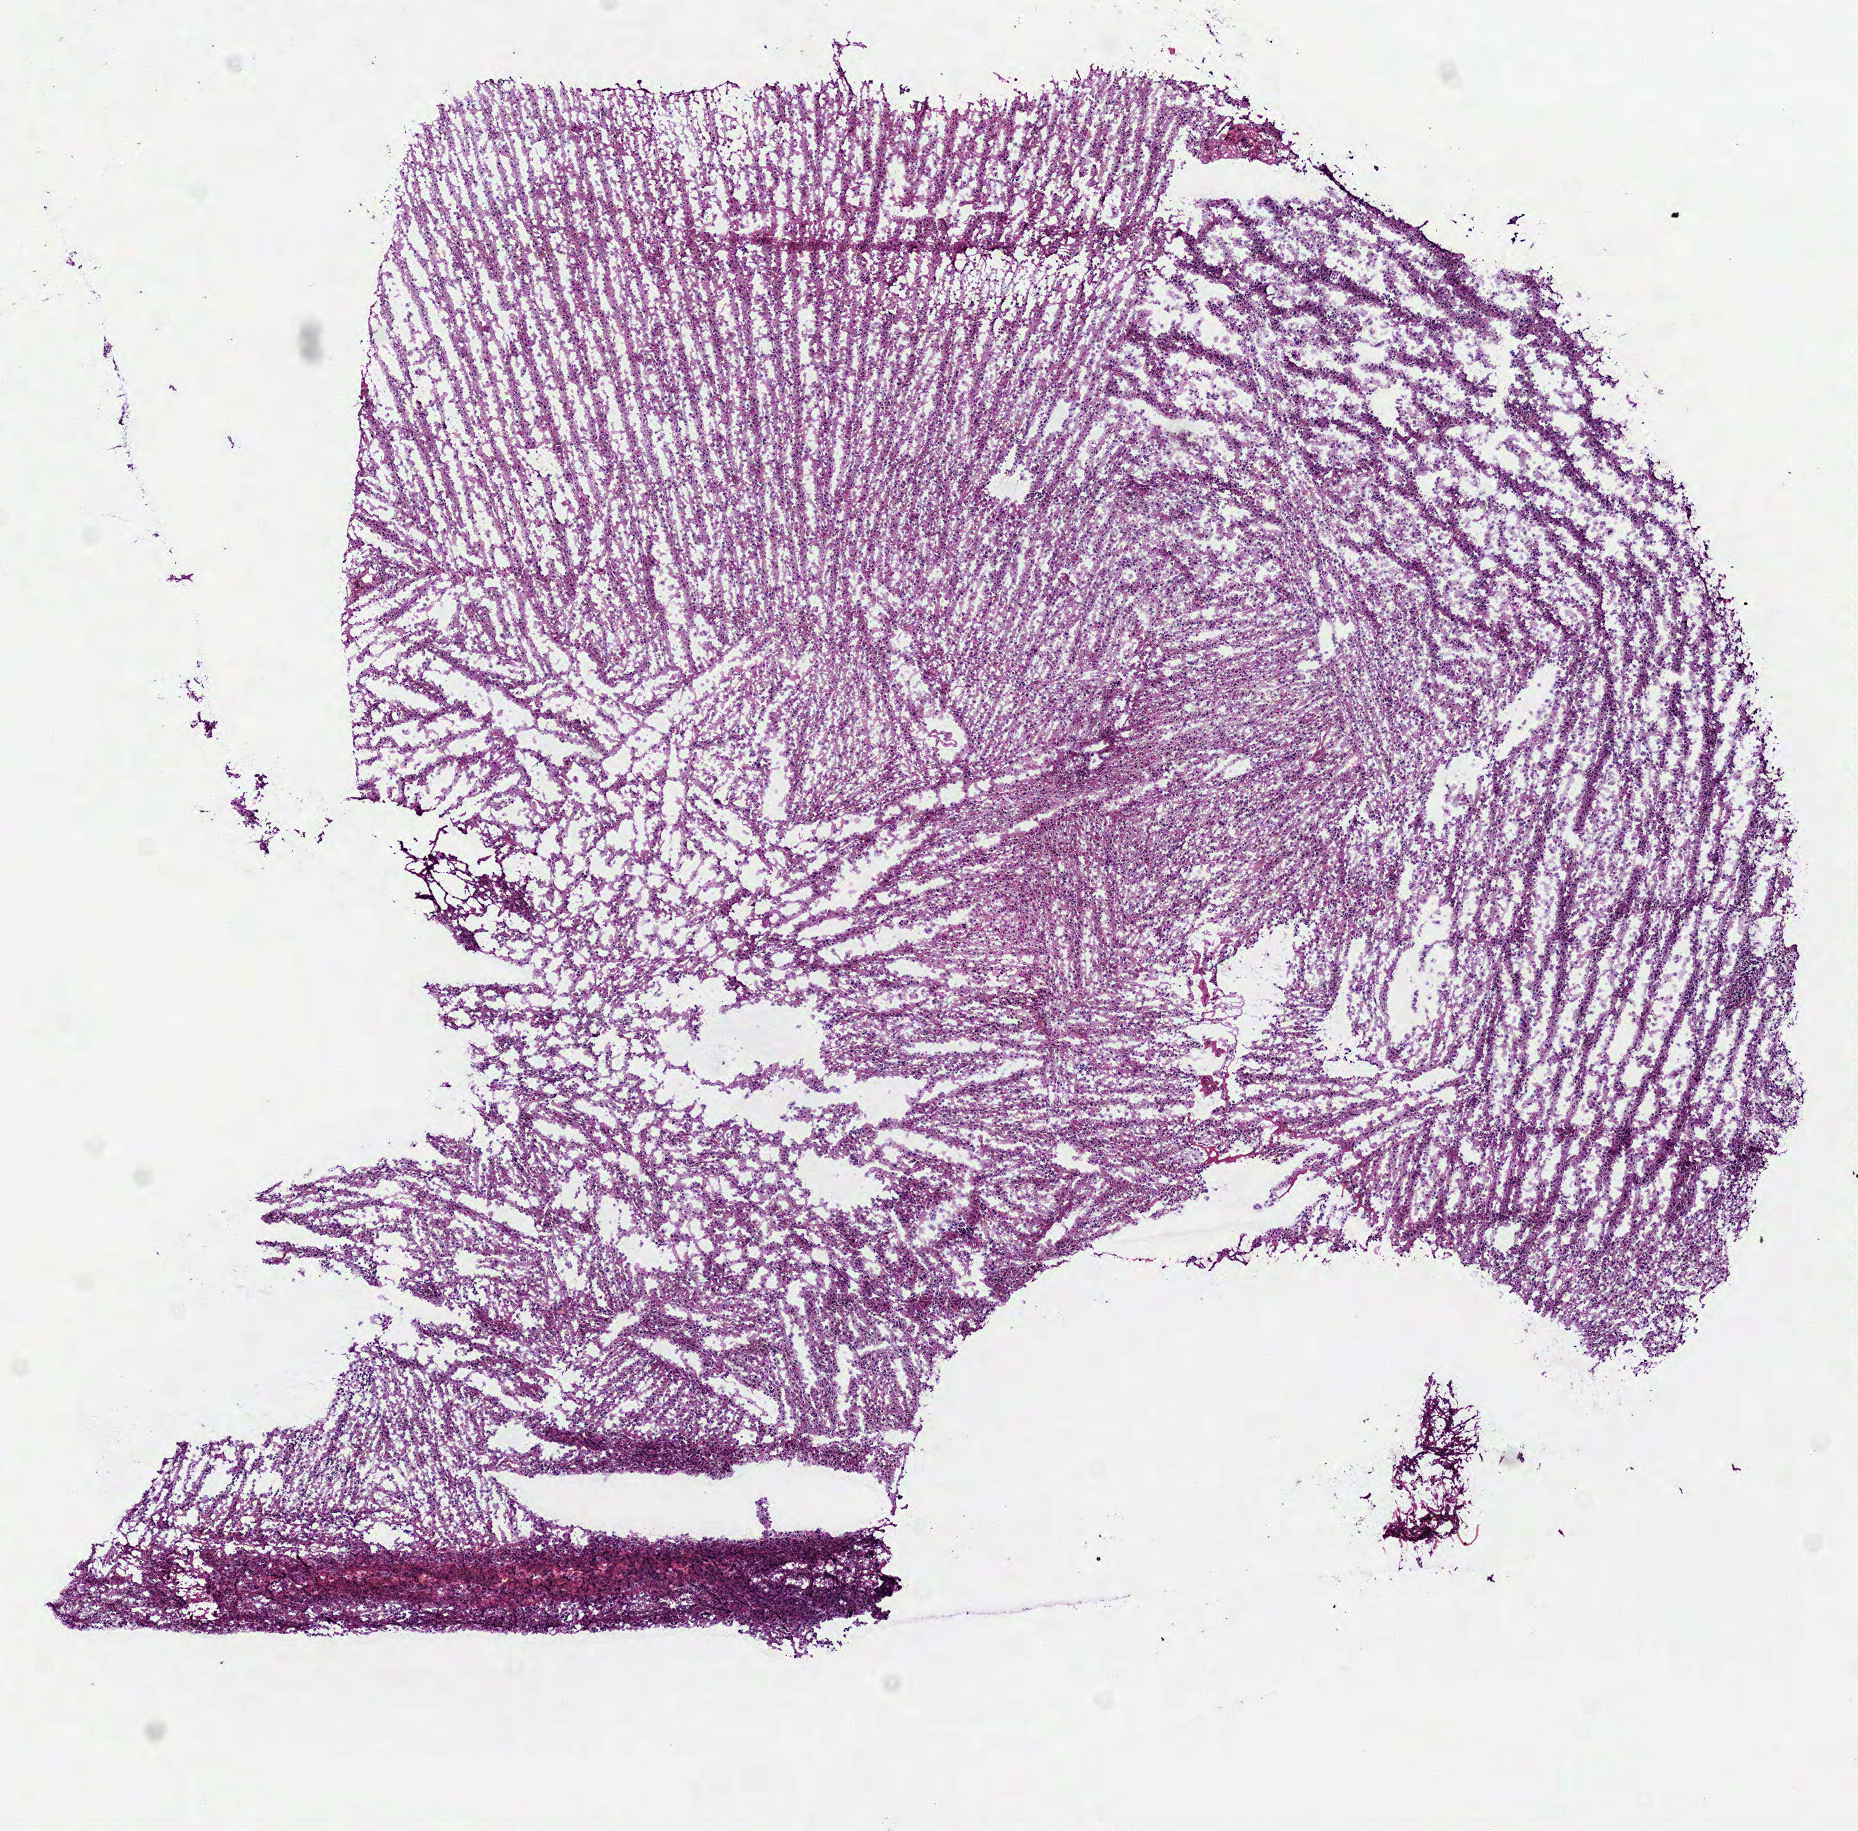
Whole-slide histology image, H&E-stained — whole scanned area (about 7.5 x 7.4 mm) shown as a low-resolution overview; frozen section from the bottom of the tissue portion; sample: primary tumour, brain. Patient: male, age at initial diagnosis 43 years. Histologic grade: G2 (moderately differentiated). Slide review estimates, as recorded: tumour cells 100%, tumour nuclei 80%, normal cells 0%, stromal cells 0%, necrosis 0%.
- histologic diagnosis: Oligodendroglioma, NOS (cerebrum)